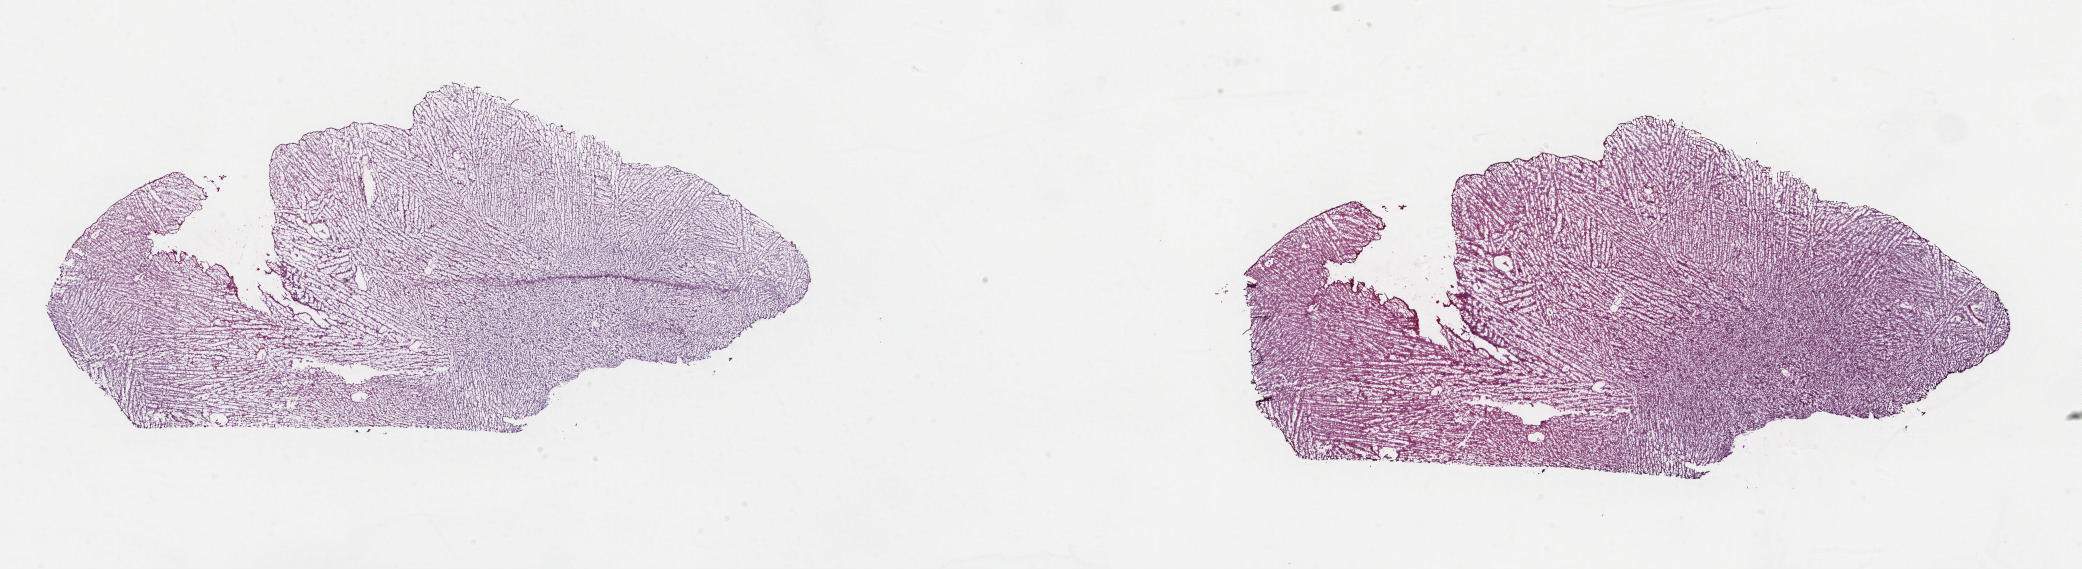
Digitized H&E tissue section (whole slide) — a low-resolution overview of the entire scanned area, about 32.9 x 9.0 mm (slide scanned at 40x). Frozen section from the top of the tissue portion. Brain, primary tumour sample. Patient: female, age at initial diagnosis 36 years. Histologic grade: G2 (moderately differentiated). Slide review estimates, as recorded: tumour cells 35%, tumour nuclei 75%, normal cells 10%, stromal cells 55%, necrosis 0%. Infiltration values recorded for this section: lymphocyte infiltration 0%, monocyte infiltration 0%, neutrophil infiltration 0%.
Laterality: right. Pathologic diagnosis: Astrocytoma, NOS (cerebrum).